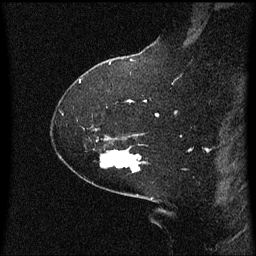
Breast MRI (dynamic contrast-enhanced), one sagittal slice. Slice 43 of 60 in the series (ordered by position). Dynamic contrast-enhanced series, image 2 of 3 at this slice position (ordered by acquisition). 1.5 T. TE 4.2 ms, TR 8 ms. 2.1 mm slice thickness. 256 × 256 image matrix, field of view 200 × 200 mm. Female patient, age 59 years.
Structures marked on this image (semi-automatically segmented with operator editing):
- analysis volume of interest (the breast-tissue region the enhancement analysis was run in; not a lesion): bounding box <100,148,143,173> (left, top, right, bottom; pixels)
- tumour enhancement mask (voxels above the 70 % enhancement threshold inside the analysis volume of interest): <134,162,139,165>